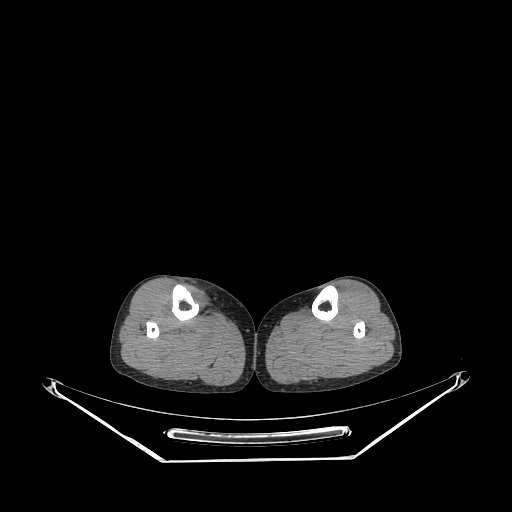
CT of an extremity soft-tissue mass (from a PET/CT study), one axial slice; slice 134 of 267 in the series (ordered by position); soft-tissue window (W 400 / L 40 HU); 3.75 mm slice thickness; 512 × 512 image matrix, field of view 500 × 500 mm. Female patient. Case-level facts recorded for this patient, not image findings: histological type: undifferentiated – high grade; grade: high; site of the primary tumour: right thigh.
Annotated regions visible in this slice (expert contour drawn on MRI and transferred to this co-registered scan by the dataset authors):
- gross tumour volume (mass): bounding box [x1, y1, x2, y2] px = [185, 285, 209, 311]